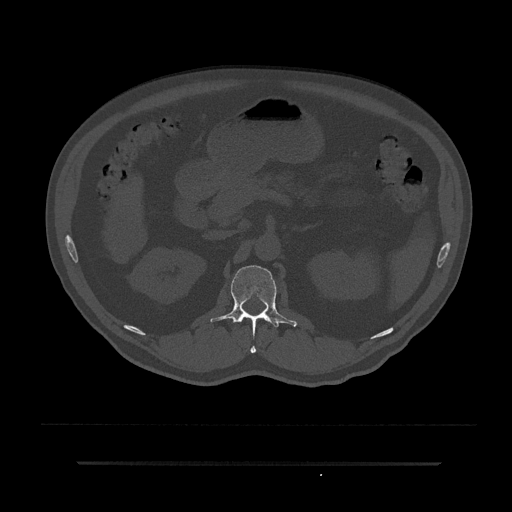
CT including the spine, one axial slice; position 150 of 797 along the scan axis; reconstruction kernel Br40s/3; 120 kVp; bone window (W 1800 / L 400 HU); 0.5 mm slice thickness; 512 × 512 image matrix. Male patient, age 59 years. From the clinical record (not read from this slice): primary cancer: bile ducts; vertebrae with lytic lesions (as recorded): T10.
Structures marked on this image (semi-automatic segmentation, software-assisted and operator-edited):
- L1 vertebra: box from (x=210, y=265) to (x=297, y=353) px